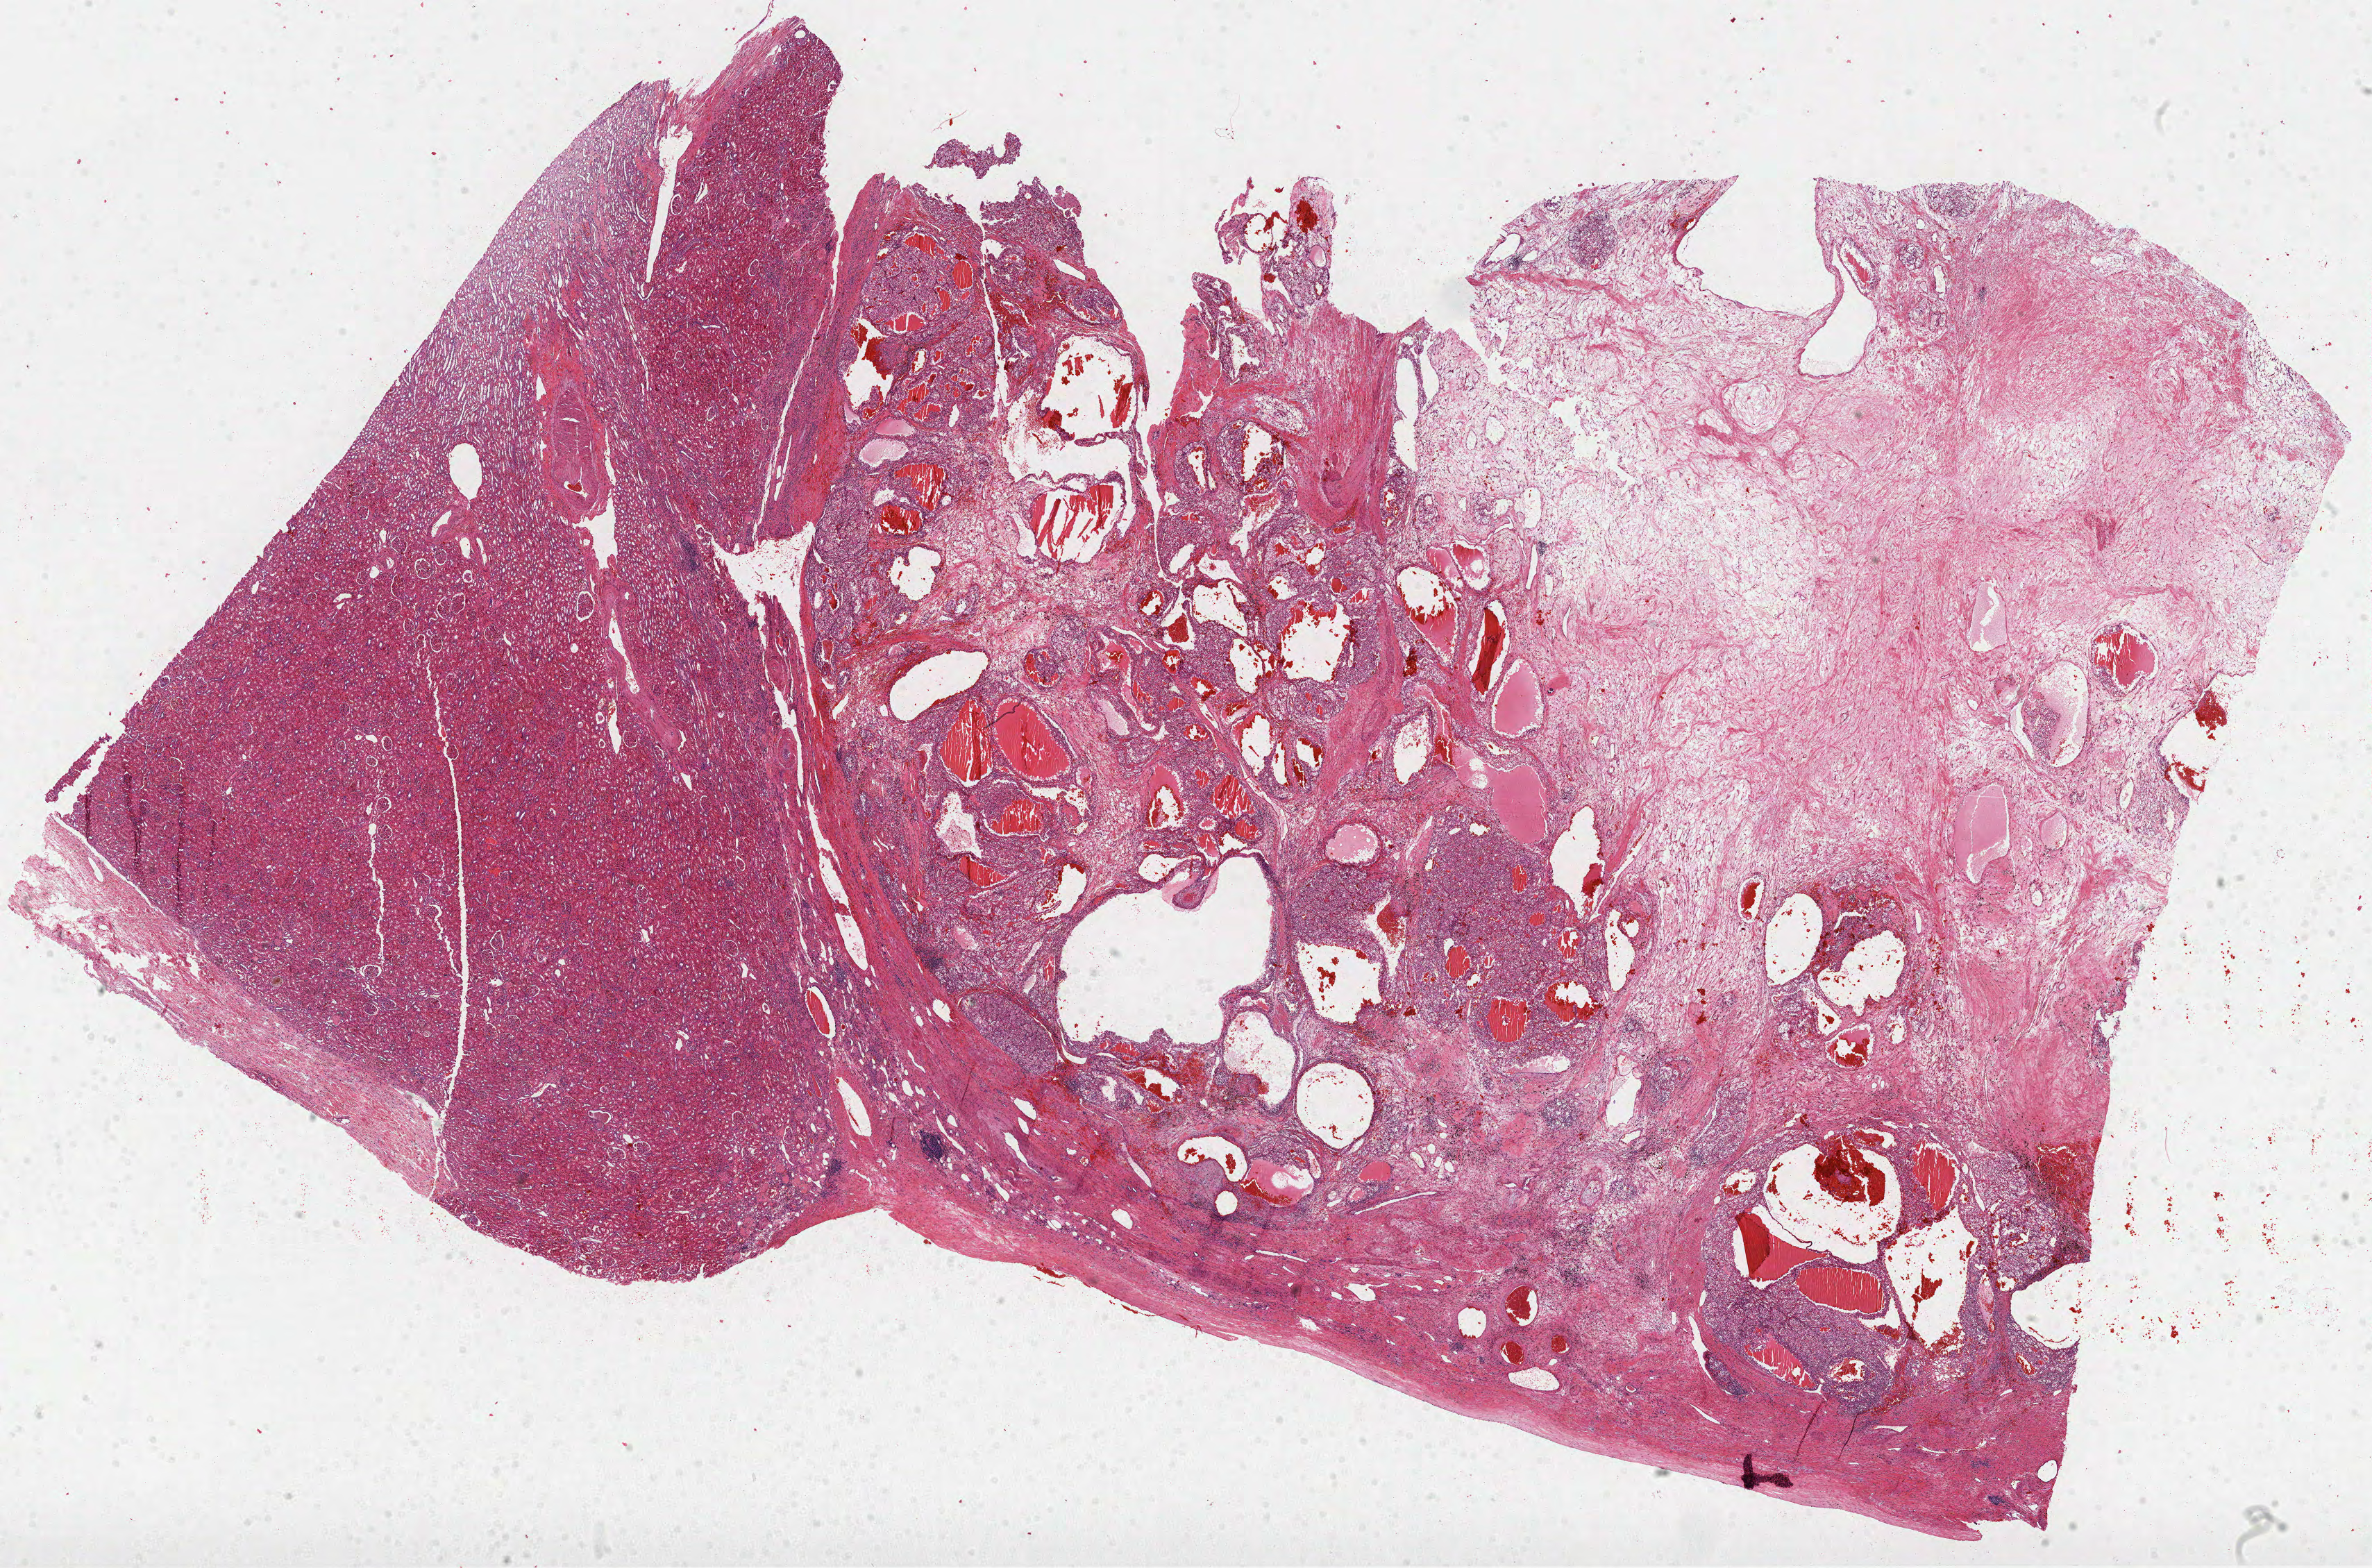
Whole-slide histology image, H&E-stained — shown as a low-resolution overview of the whole scanned area (about 27.6 x 18.2 mm, slide scanned at 40x), FFPE section, sample: primary tumour, kidney. Male, age 71 years at initial diagnosis. Histologic grade: G2 (moderately differentiated).
- AJCC pathologic stage: I (6th edition)
- pathologic diagnosis: Clear cell adenocarcinoma, NOS
- laterality: left